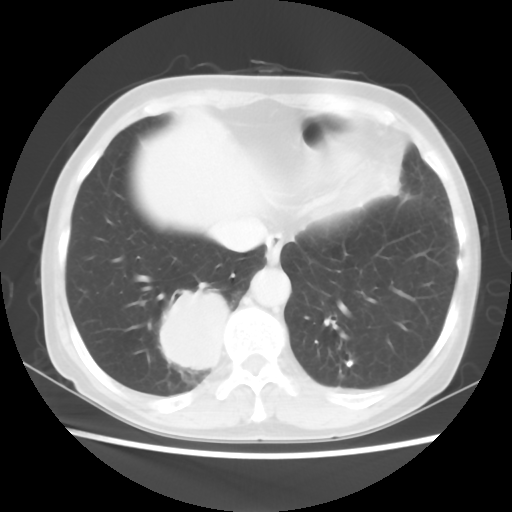
Chest CT, one axial slice. Slice 14 of 56 in the series (ordered by position). Lung window (W 1500 / L -600 HU). 5 mm slice thickness. 512 × 512 image matrix. Female patient, age 66 years. From the clinical record (not read from this slice): clinical TNM (as recorded): T2 N3 M0; histopathological grade: G3.
Structures marked on this image (rectangle marked by the reading radiologist):
- lung tumour (recorded histology: small cell carcinoma): bounding box (x1, y1, x2, y2) in pixels: (152, 279, 230, 377)